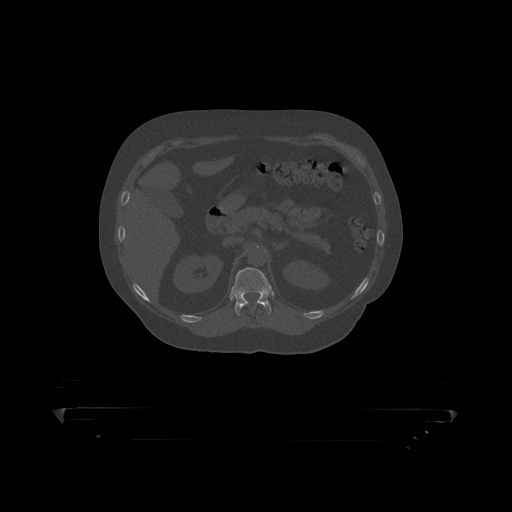
CT including the spine, one axial slice. Slice 178 of 390 in the series (ordered by position). Reconstruction kernel STANDARD. 120 kVp. Bone window (W 1800 / L 400 HU). 512 × 512 image matrix, field of view 650 × 650 mm. Patient: male, 60 years. From the clinical record (not read from this slice): primary cancer: prostate.
Annotated regions visible in this slice (semi-automatic segmentation, software-assisted and operator-edited):
- T11 vertebra: box from (x=255, y=305) to (x=266, y=311) px
- T12 vertebra: (x=232, y=268)–(x=272, y=316)